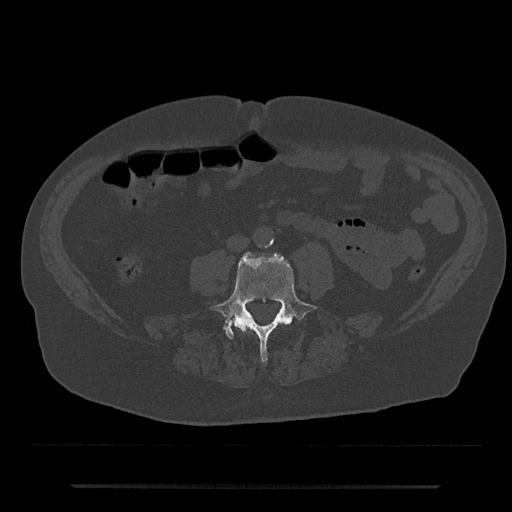
CT including the spine, one axial slice. Slice 354 of 797 in the series (ordered by position). Bone window (W 1800 / L 400 HU). 0.5 mm slice thickness. 512 × 512 image matrix, field of view 434 × 434 mm. Male patient, age 80 years. Case-level facts recorded for this patient, not image findings: primary cancer: prostate; vertebrae with lytic lesions (as recorded): L1, T11.
Annotated regions visible in this slice (semi-automatic segmentation, software-assisted and operator-edited):
- L3 vertebra: bounding box (x1, y1, x2, y2) in pixels: (244, 321, 250, 326)
- L4 vertebra: (209, 252, 317, 363)